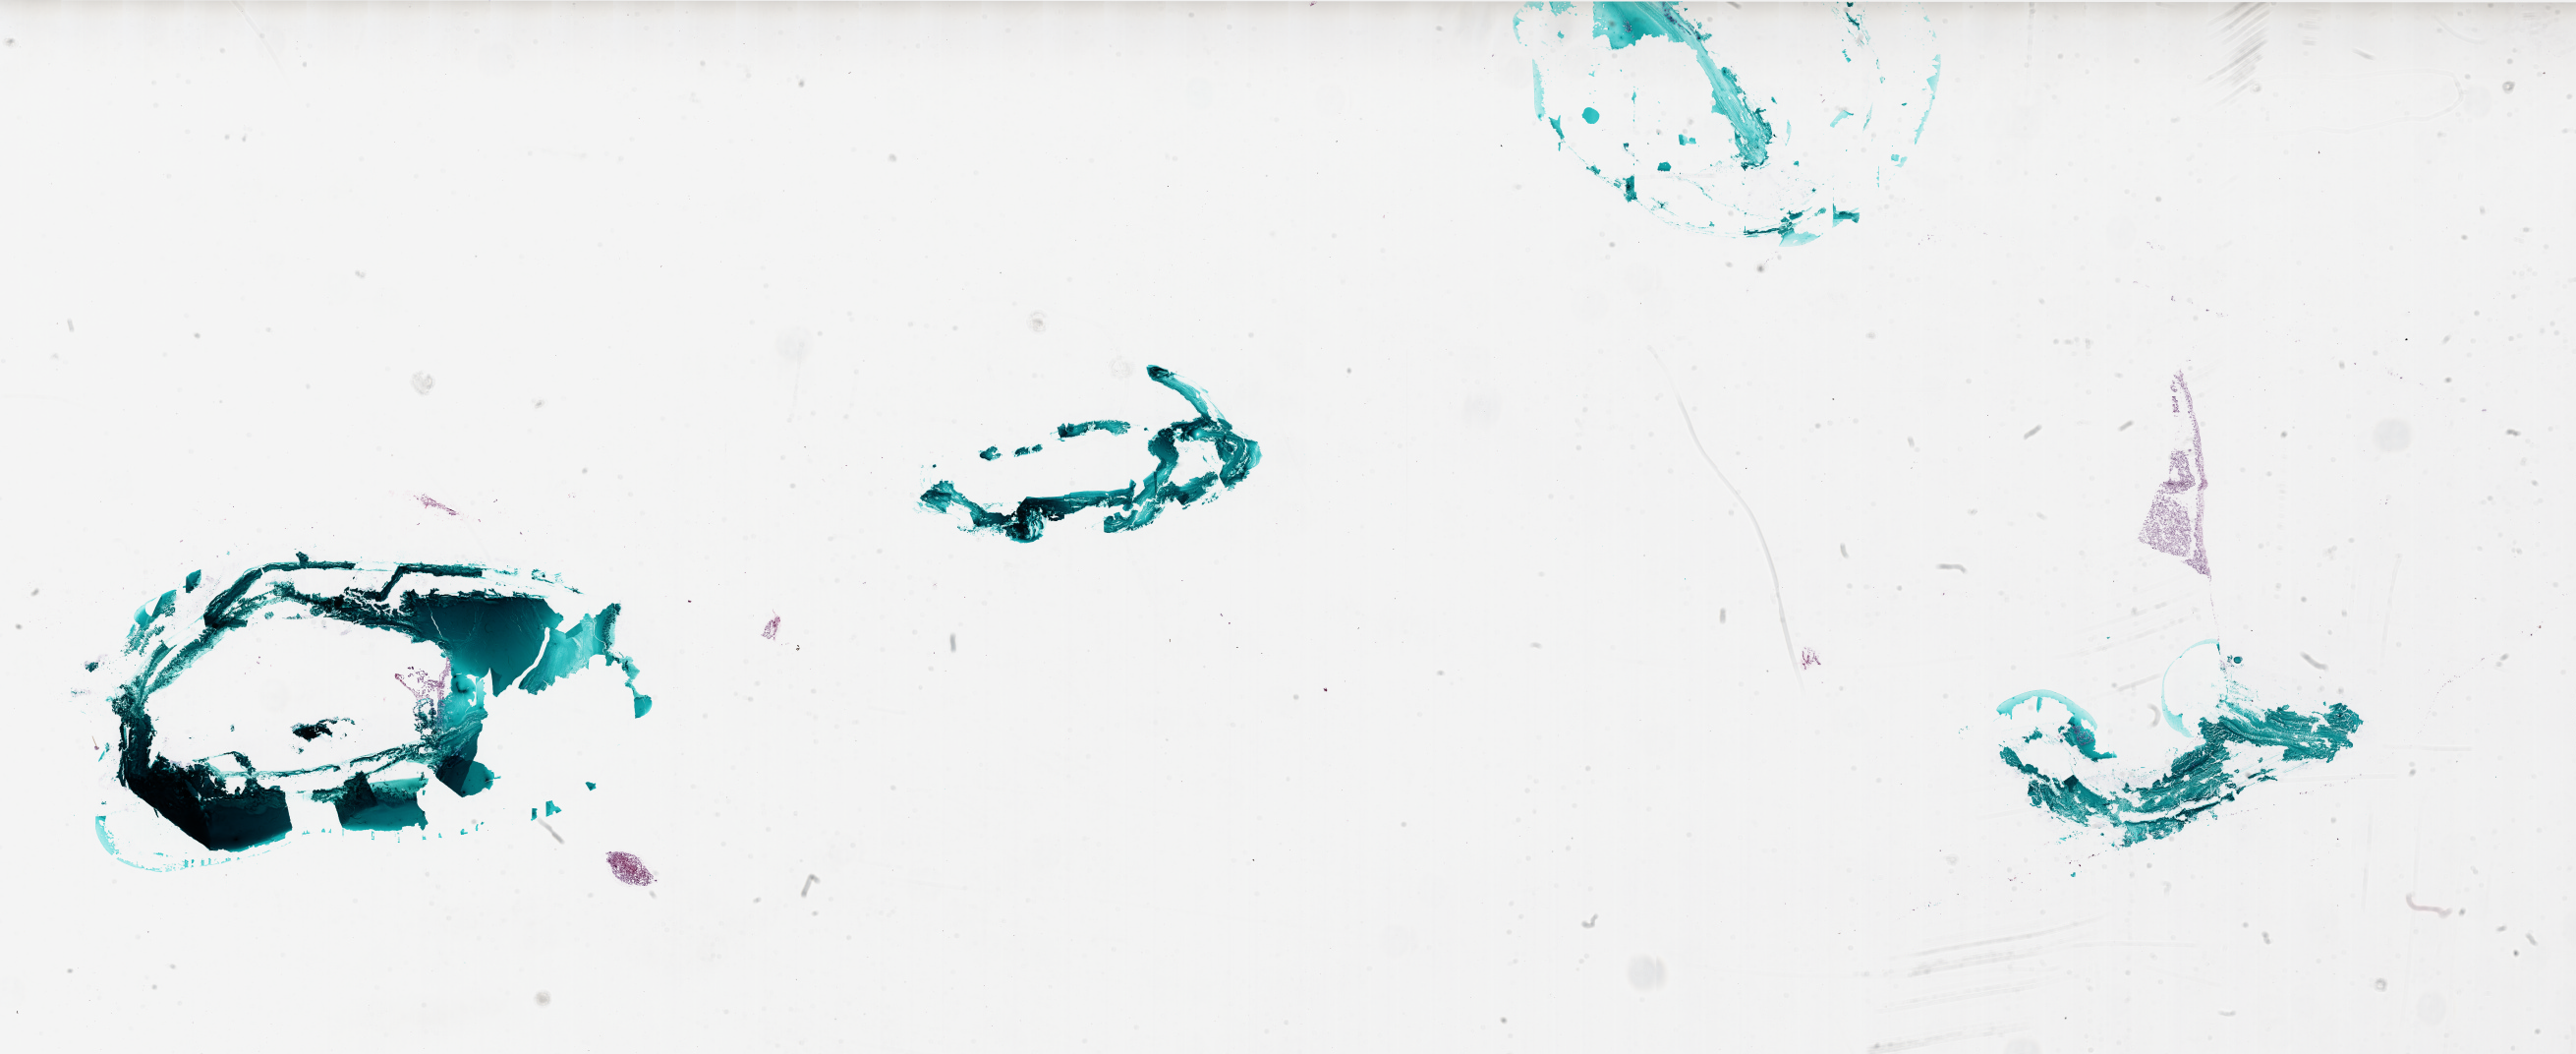
Digitized H&E-stained tissue section (whole slide), low-resolution overview of the scanned area, about 42.0 x 17.2 mm (slide scanned at 20x), frozen section from the bottom of the tissue portion, sample: primary tumour, brain. Female patient; age at initial diagnosis 31 years. Composition of this section per pathologist review: tumour cells 100%, tumour nuclei 100%, normal cells 0%, stromal cells 0%, necrosis 0%.
Pathologic diagnosis: Glioblastoma.